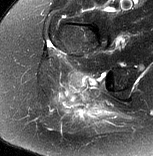
MRI of an extremity soft-tissue mass, one axial slice; slice 54 of 77 in the series (ordered by position); T2-weighted fat-saturated; MR volume resampled by the dataset authors to the PET/CT grid (not the native acquisition matrix); 153 × 156 image matrix. Female patient. From the clinical record (not read from this slice): histological type: synovial sarcoma; grade: intermediate; site of the primary tumour: right buttock.
Outlined on this slice (expert contour drawn on MRI and transferred to this co-registered scan by the dataset authors):
- gross tumour volume including surrounding oedema: bounding box <58,74,113,121> (left, top, right, bottom; pixels)